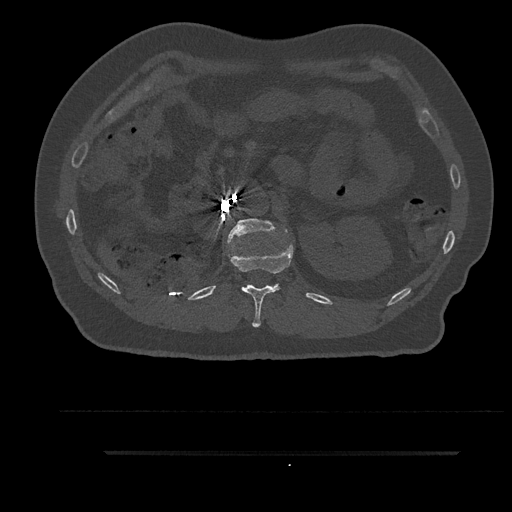
CT including the spine, one axial slice; slice 222 of 797 in the series (ordered by position); reconstruction kernel Br40s/3; 120 kVp; bone window (W 1800 / L 400 HU); 0.5 mm slice thickness; 512 × 512 image matrix, field of view 432 × 432 mm. Patient: male, 63 years. Case-level facts recorded for this patient, not image findings: primary cancer: renal; vertebrae with lytic lesions (as recorded): T8.
Structures marked on this image (semi-automatic segmentation, software-assisted and operator-edited):
- L1 vertebra: bounding box [x1, y1, x2, y2] px = [226, 218, 288, 245]
- T12 vertebra: [227, 234, 294, 328]